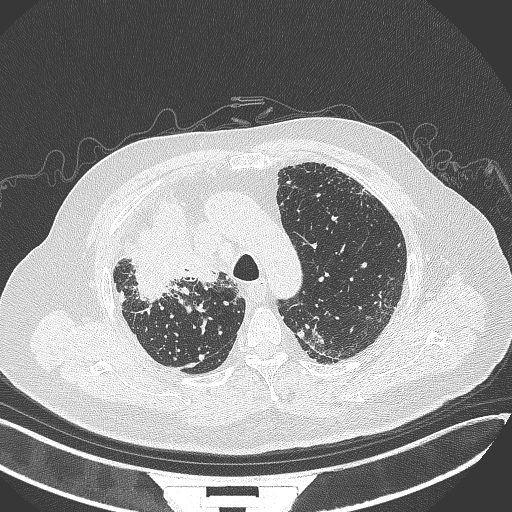
Chest CT, one axial slice. Position 268 of 384 along the scan axis. 120 kVp. Lung window (W 1500 / L -600 HU). 1 mm slice thickness. 512 × 512 image matrix. Male patient, age 69 years. Case-level facts recorded for this patient, not image findings: clinical TNM (as recorded): T4 N3 M1.
Annotated regions visible in this slice (rectangle marked by the reading radiologist):
- lung tumour (recorded histology: adenocarcinoma): bounding box <127,203,221,303> (left, top, right, bottom; pixels)